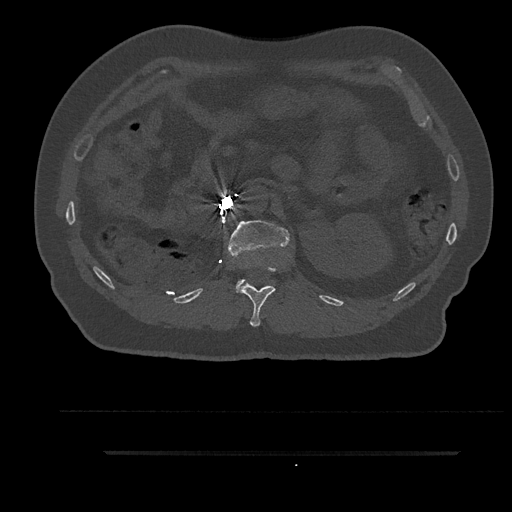
CT including the spine, one axial slice. Position 211 of 797 along the scan axis. Reconstruction kernel Br40s/3. Bone window (W 1800 / L 400 HU). 0.5 mm slice thickness. 512 × 512 image matrix. Patient: male, 63 years. From the clinical record (not read from this slice): primary cancer: renal; vertebrae with lytic lesions (as recorded): T8.
Structures marked on this image (semi-automatic segmentation, software-assisted and operator-edited):
- L1 vertebra: bounding box (x1, y1, x2, y2) in pixels: (228, 220, 289, 292)
- T12 vertebra: (238, 265, 277, 327)